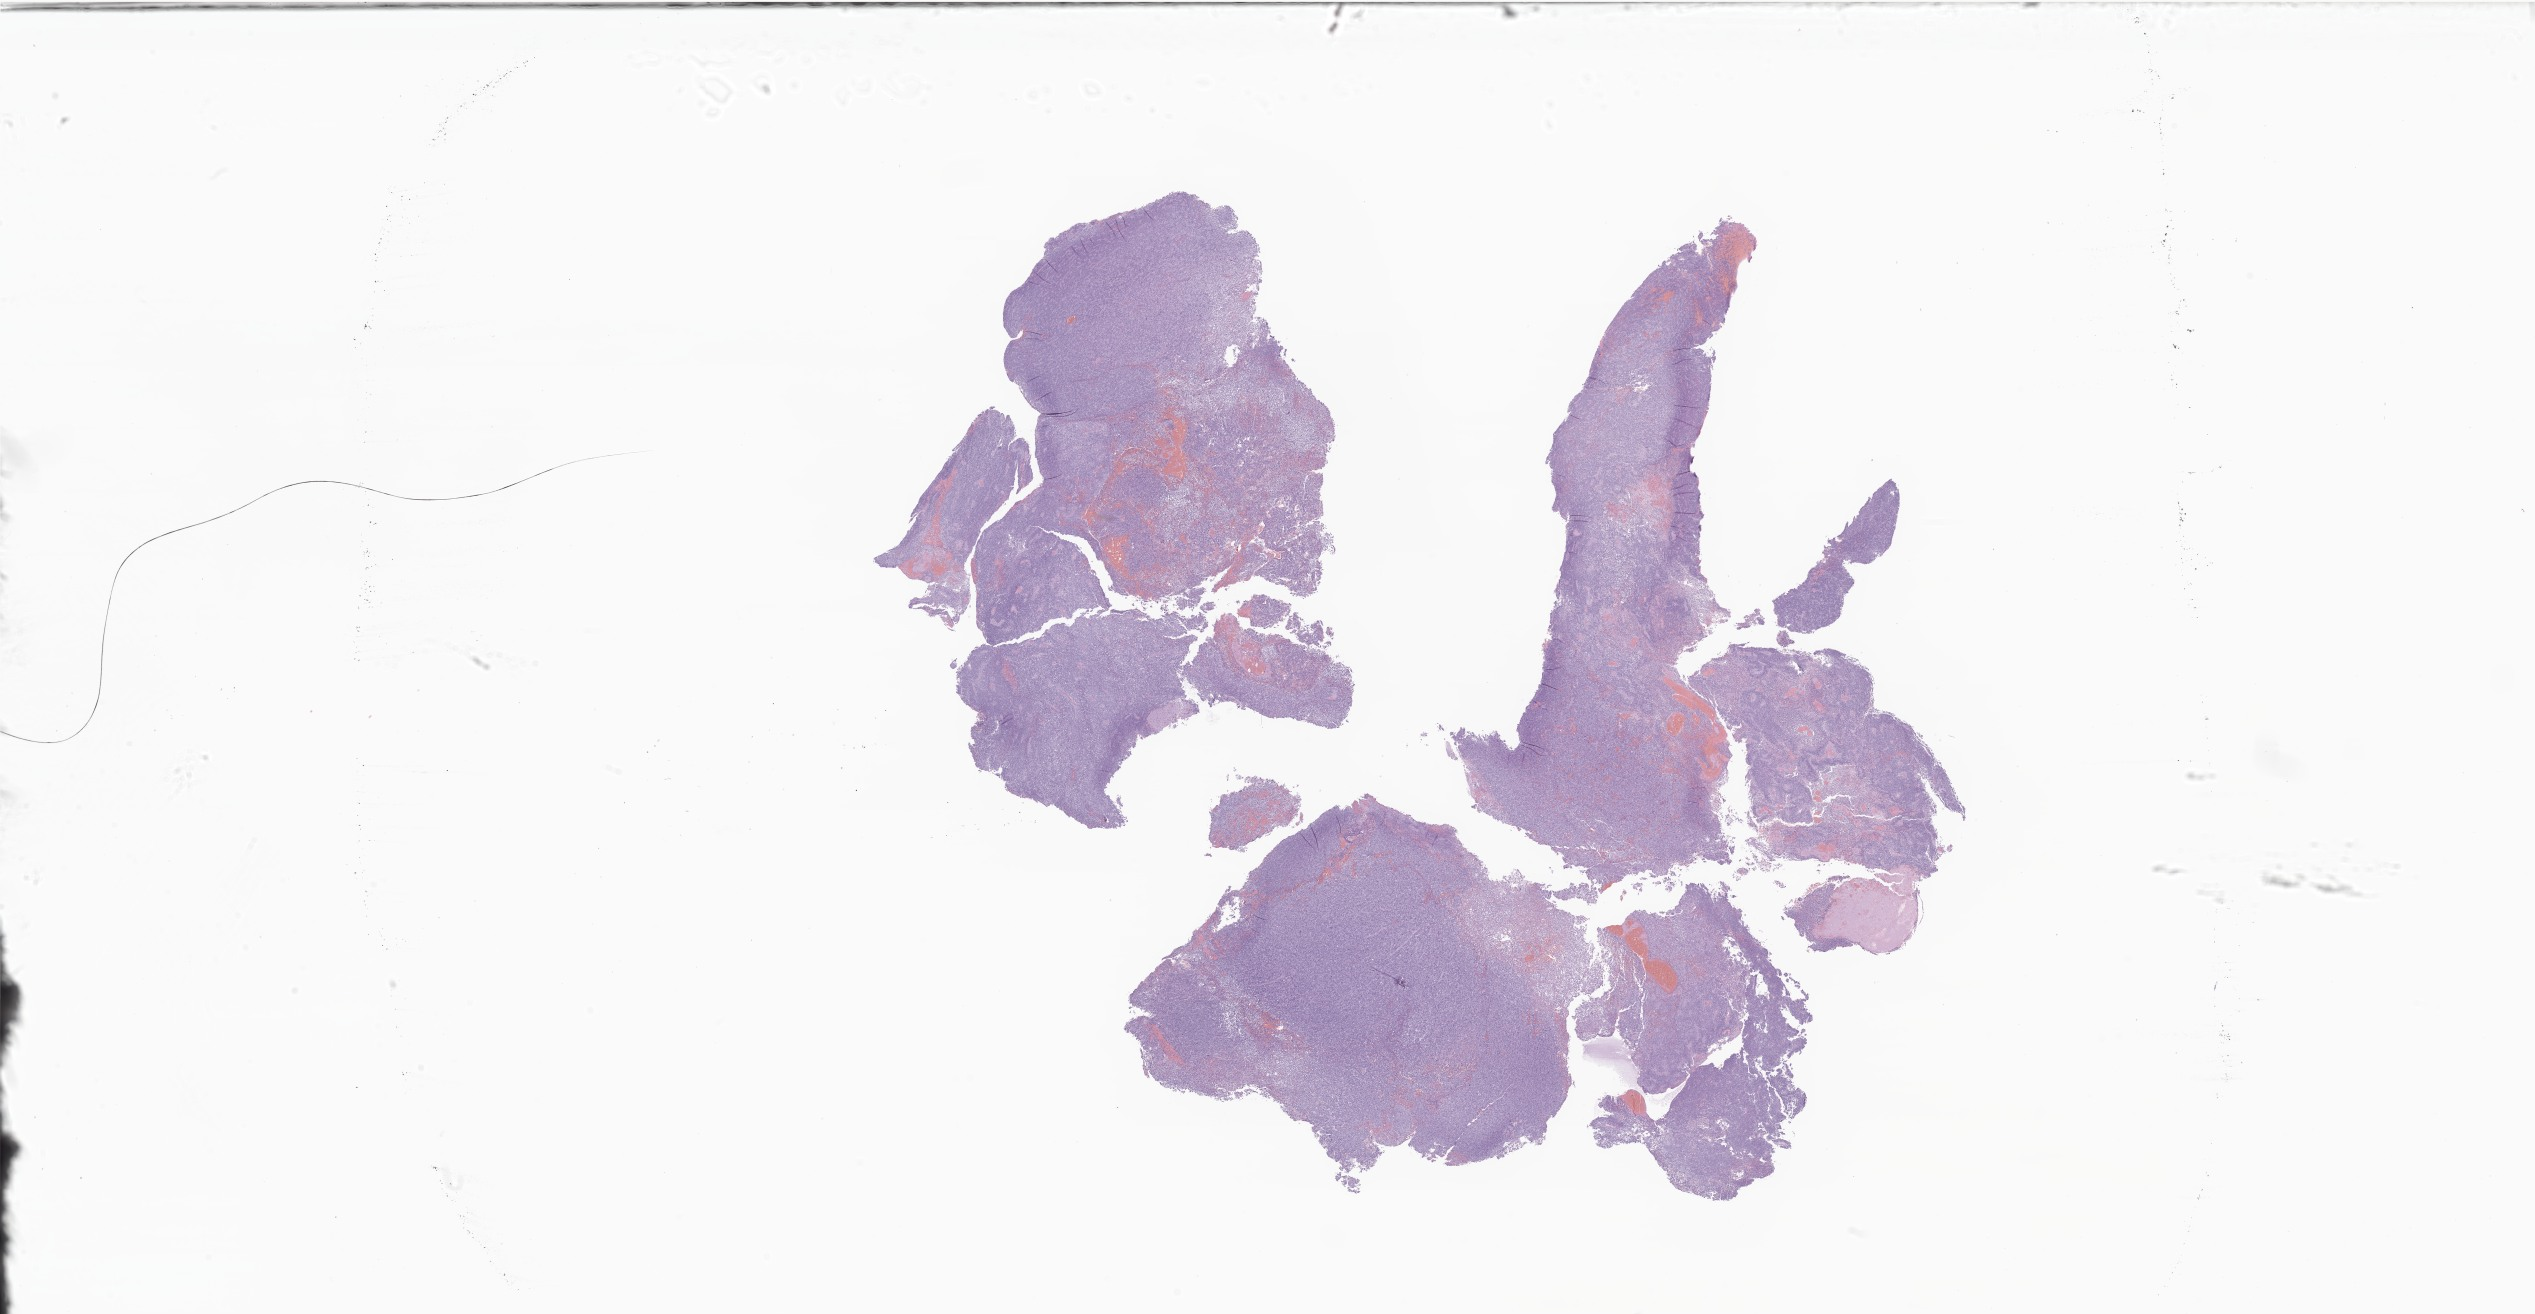
Whole-slide image, haematoxylin and eosin stain of tumor tissue from the brain — whole scanned area (about 42.7 x 22.2 mm) shown as a low-resolution overview. FFPE section. Female patient, age 54 months (4 years 6 months).
Diagnosis (ICD-O-3 morphology term): Neoplasm, uncertain whether benign or malignant.